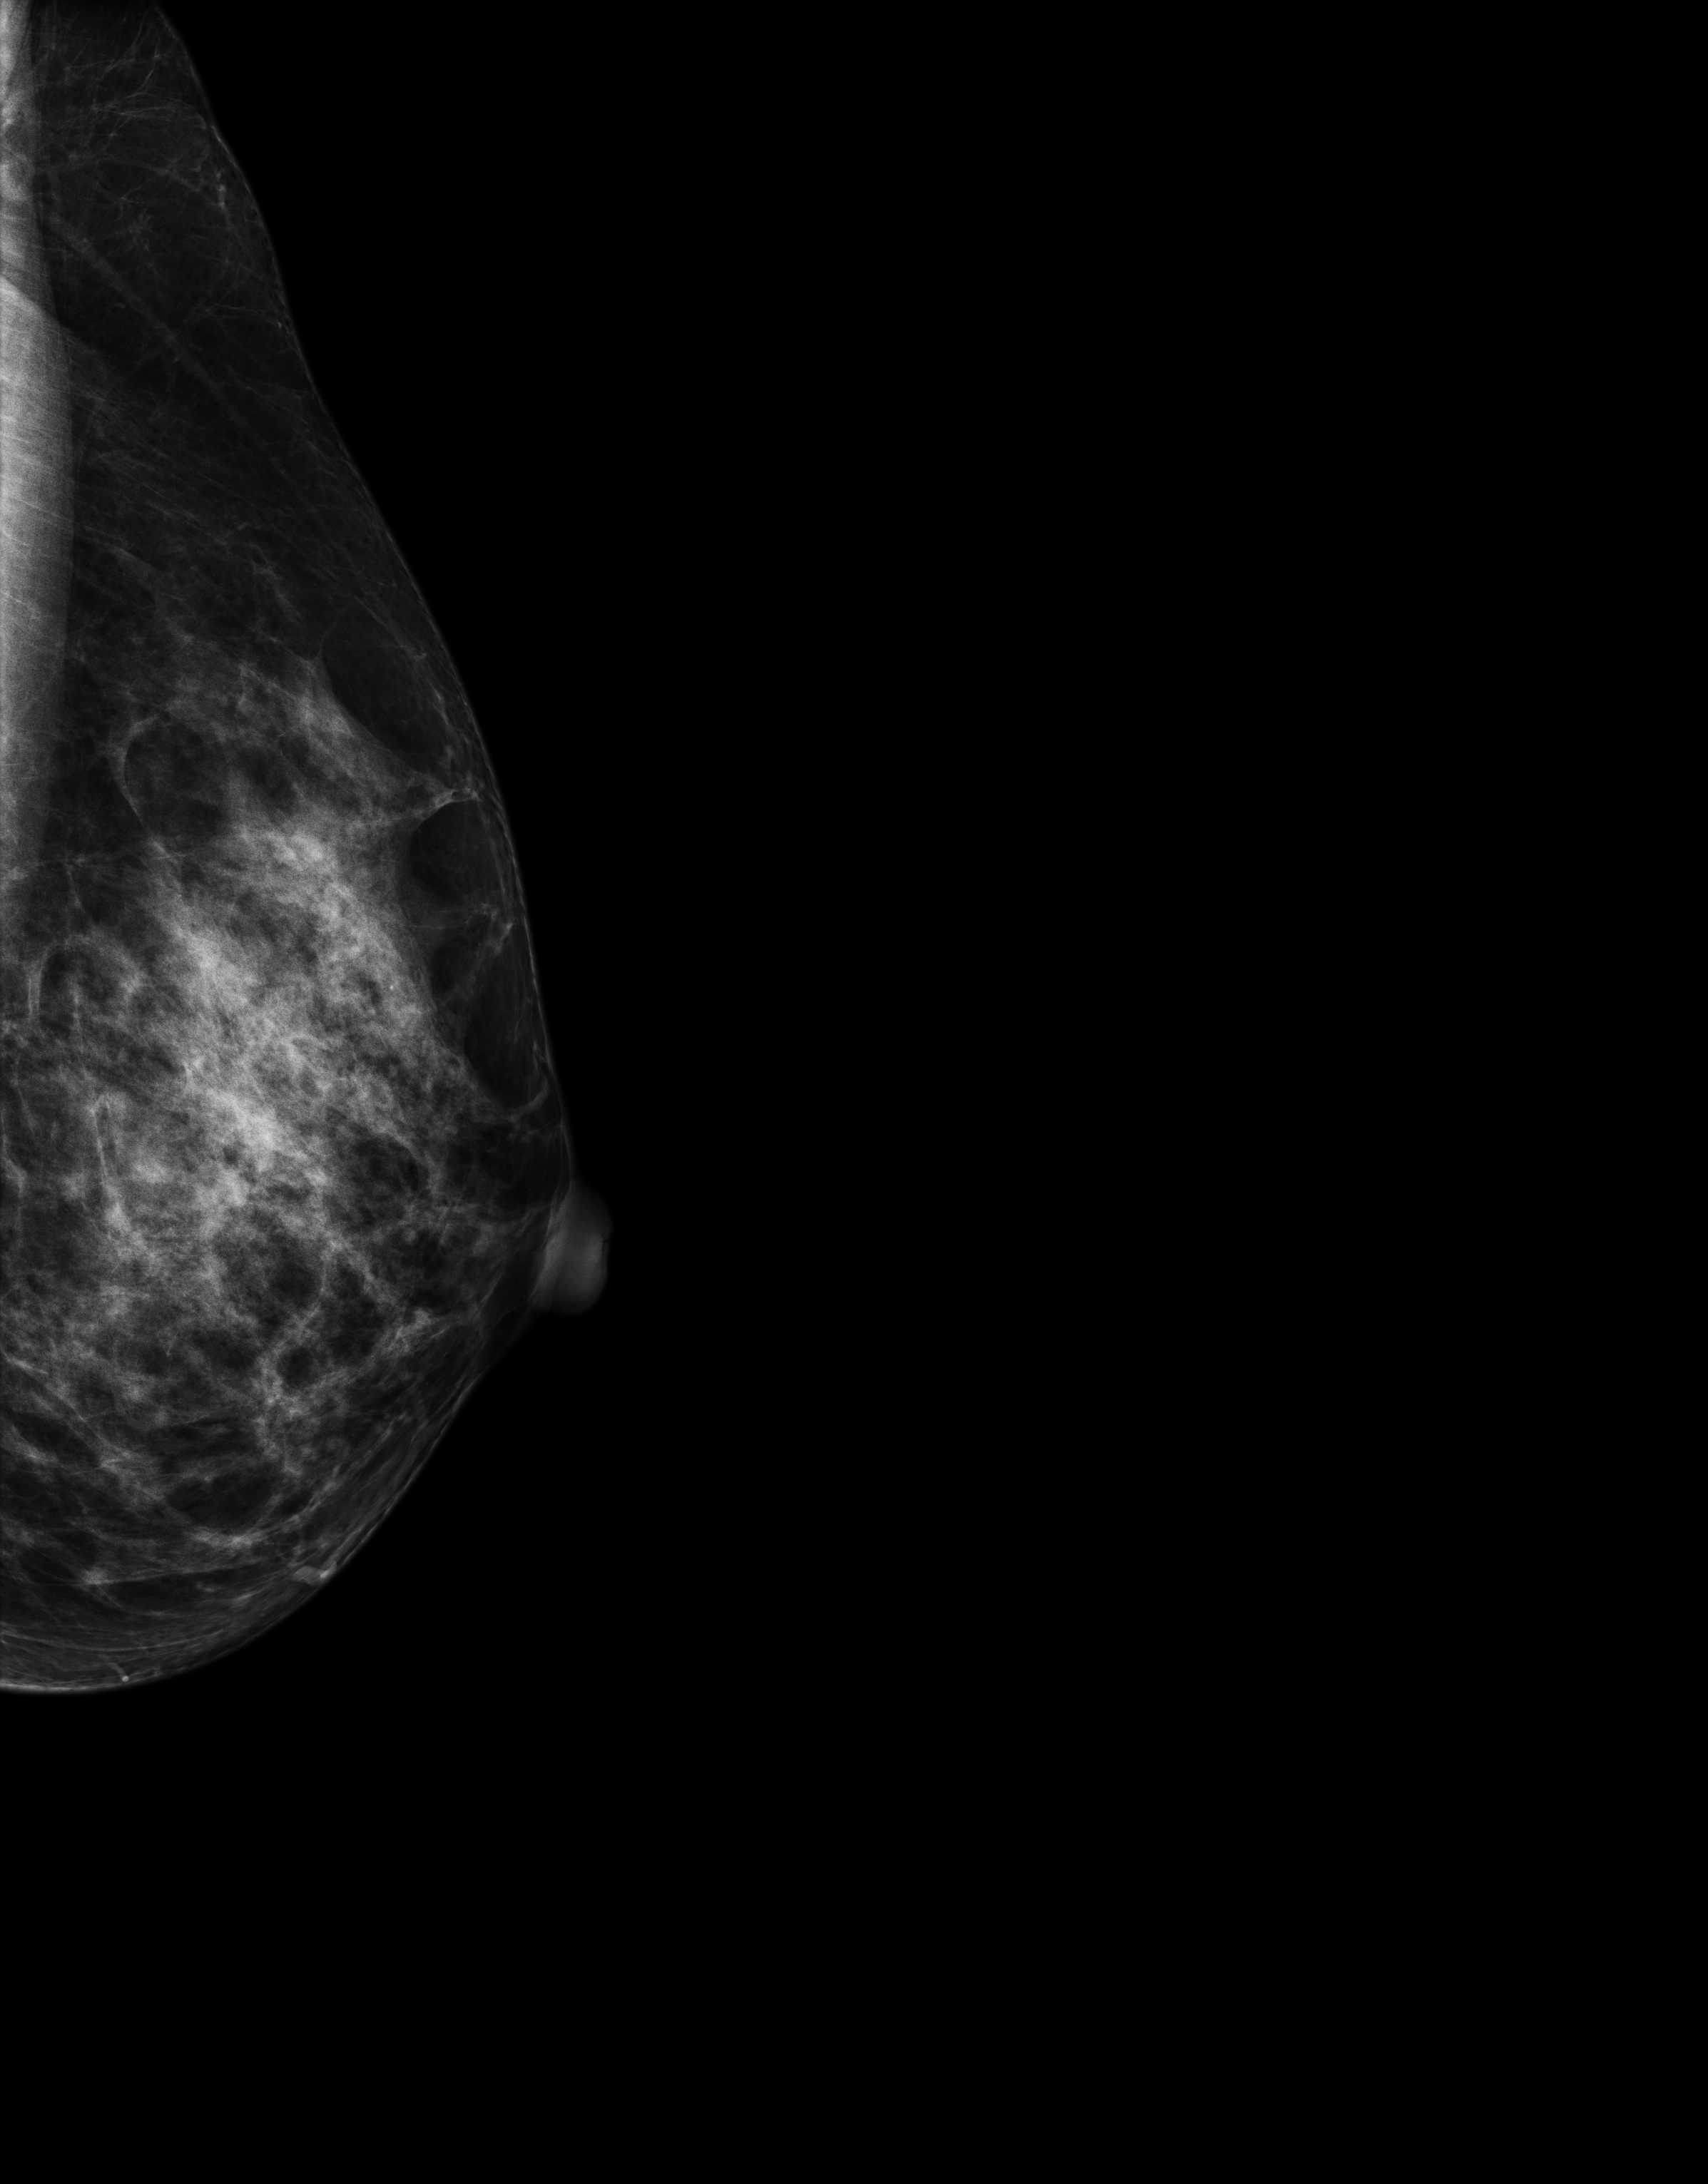
Screening examination. Patient aged 43 years (female).
Image type: full-field digital mammogram. Breast: left. Projection: exaggerated CC view (lateral).